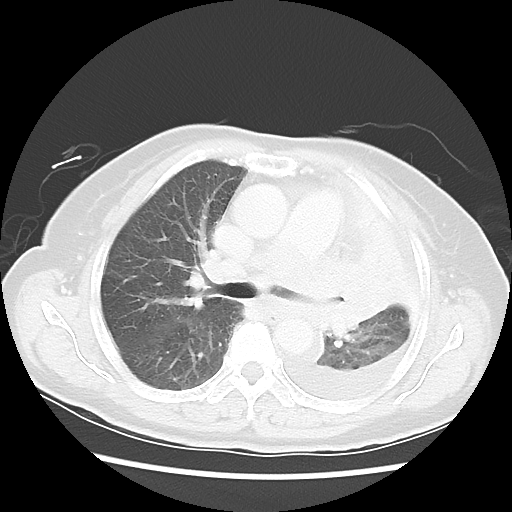
Chest CT, one axial slice. Position 34 of 52 along the scan axis. Reconstruction kernel LUNG. 120 kVp. Lung window (W 1500 / L -600 HU). 5 mm slice thickness. 512 × 512 image matrix, field of view 336 × 336 mm. Female patient, age 72 years. From the clinical record (not read from this slice): clinical TNM (as recorded): T4 N3 M1b; histopathological grade: G3.
Outlined on this slice (bounding box drawn by a radiologist):
- lung tumour (recorded histology: large cell carcinoma): bounding box [x1, y1, x2, y2] px = [308, 252, 398, 337]